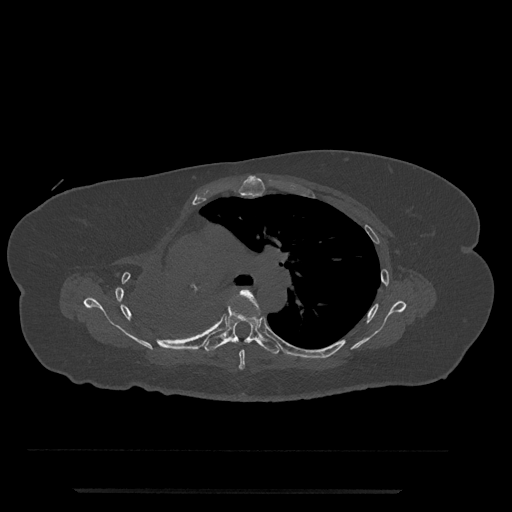
CT including the spine, one axial slice; position 513 of 797 along the scan axis; bone window (W 1800 / L 400 HU); 0.5 mm slice thickness; 512 × 512 image matrix, field of view 440 × 440 mm. Patient: female, 51 years. Case-level facts recorded for this patient, not image findings: primary cancer: neuro.
Annotated regions visible in this slice (semi-automatic segmentation, software-assisted and operator-edited):
- T5 vertebra: bounding box (x1, y1, x2, y2) in pixels: (231, 289, 265, 370)
- T6 vertebra: (205, 306, 280, 355)